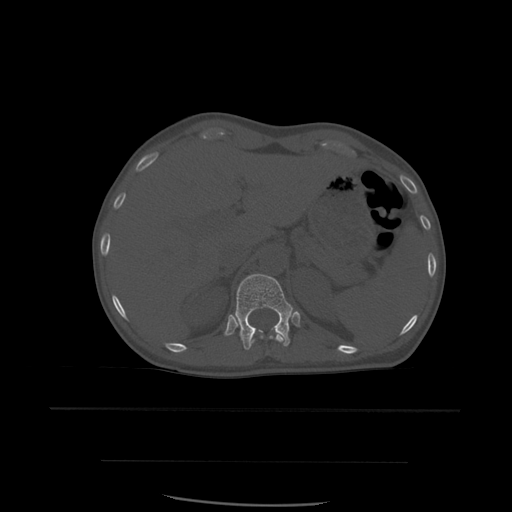
CT including the spine, one axial slice. Position 279 of 574 along the scan axis. Bone window (W 1800 / L 400 HU). 1.25 mm slice thickness. 512 × 512 image matrix, field of view 392 × 392 mm. Patient age 48 years. From the clinical record (not read from this slice): primary cancer: lung.
Annotated regions visible in this slice (semi-automatically segmented with operator editing):
- T11 vertebra: box from (x=251, y=333) to (x=285, y=346) px
- T12 vertebra: (x=235, y=274)–(x=293, y=350)